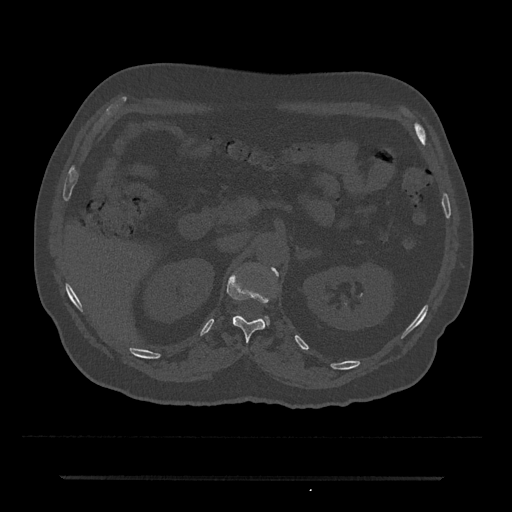
CT including the spine, one axial slice; slice 115 of 797 in the series (ordered by position); bone window (W 1800 / L 400 HU); 0.5 mm slice thickness; 512 × 512 image matrix. Patient: male, 69 years. Case-level facts recorded for this patient, not image findings: primary cancer: prostate.
Structures marked on this image (semi-automatic segmentation, software-assisted and operator-edited):
- L1 vertebra: bounding box (x1, y1, x2, y2) in pixels: (263, 268, 278, 323)
- T12 vertebra: (227, 270, 278, 341)